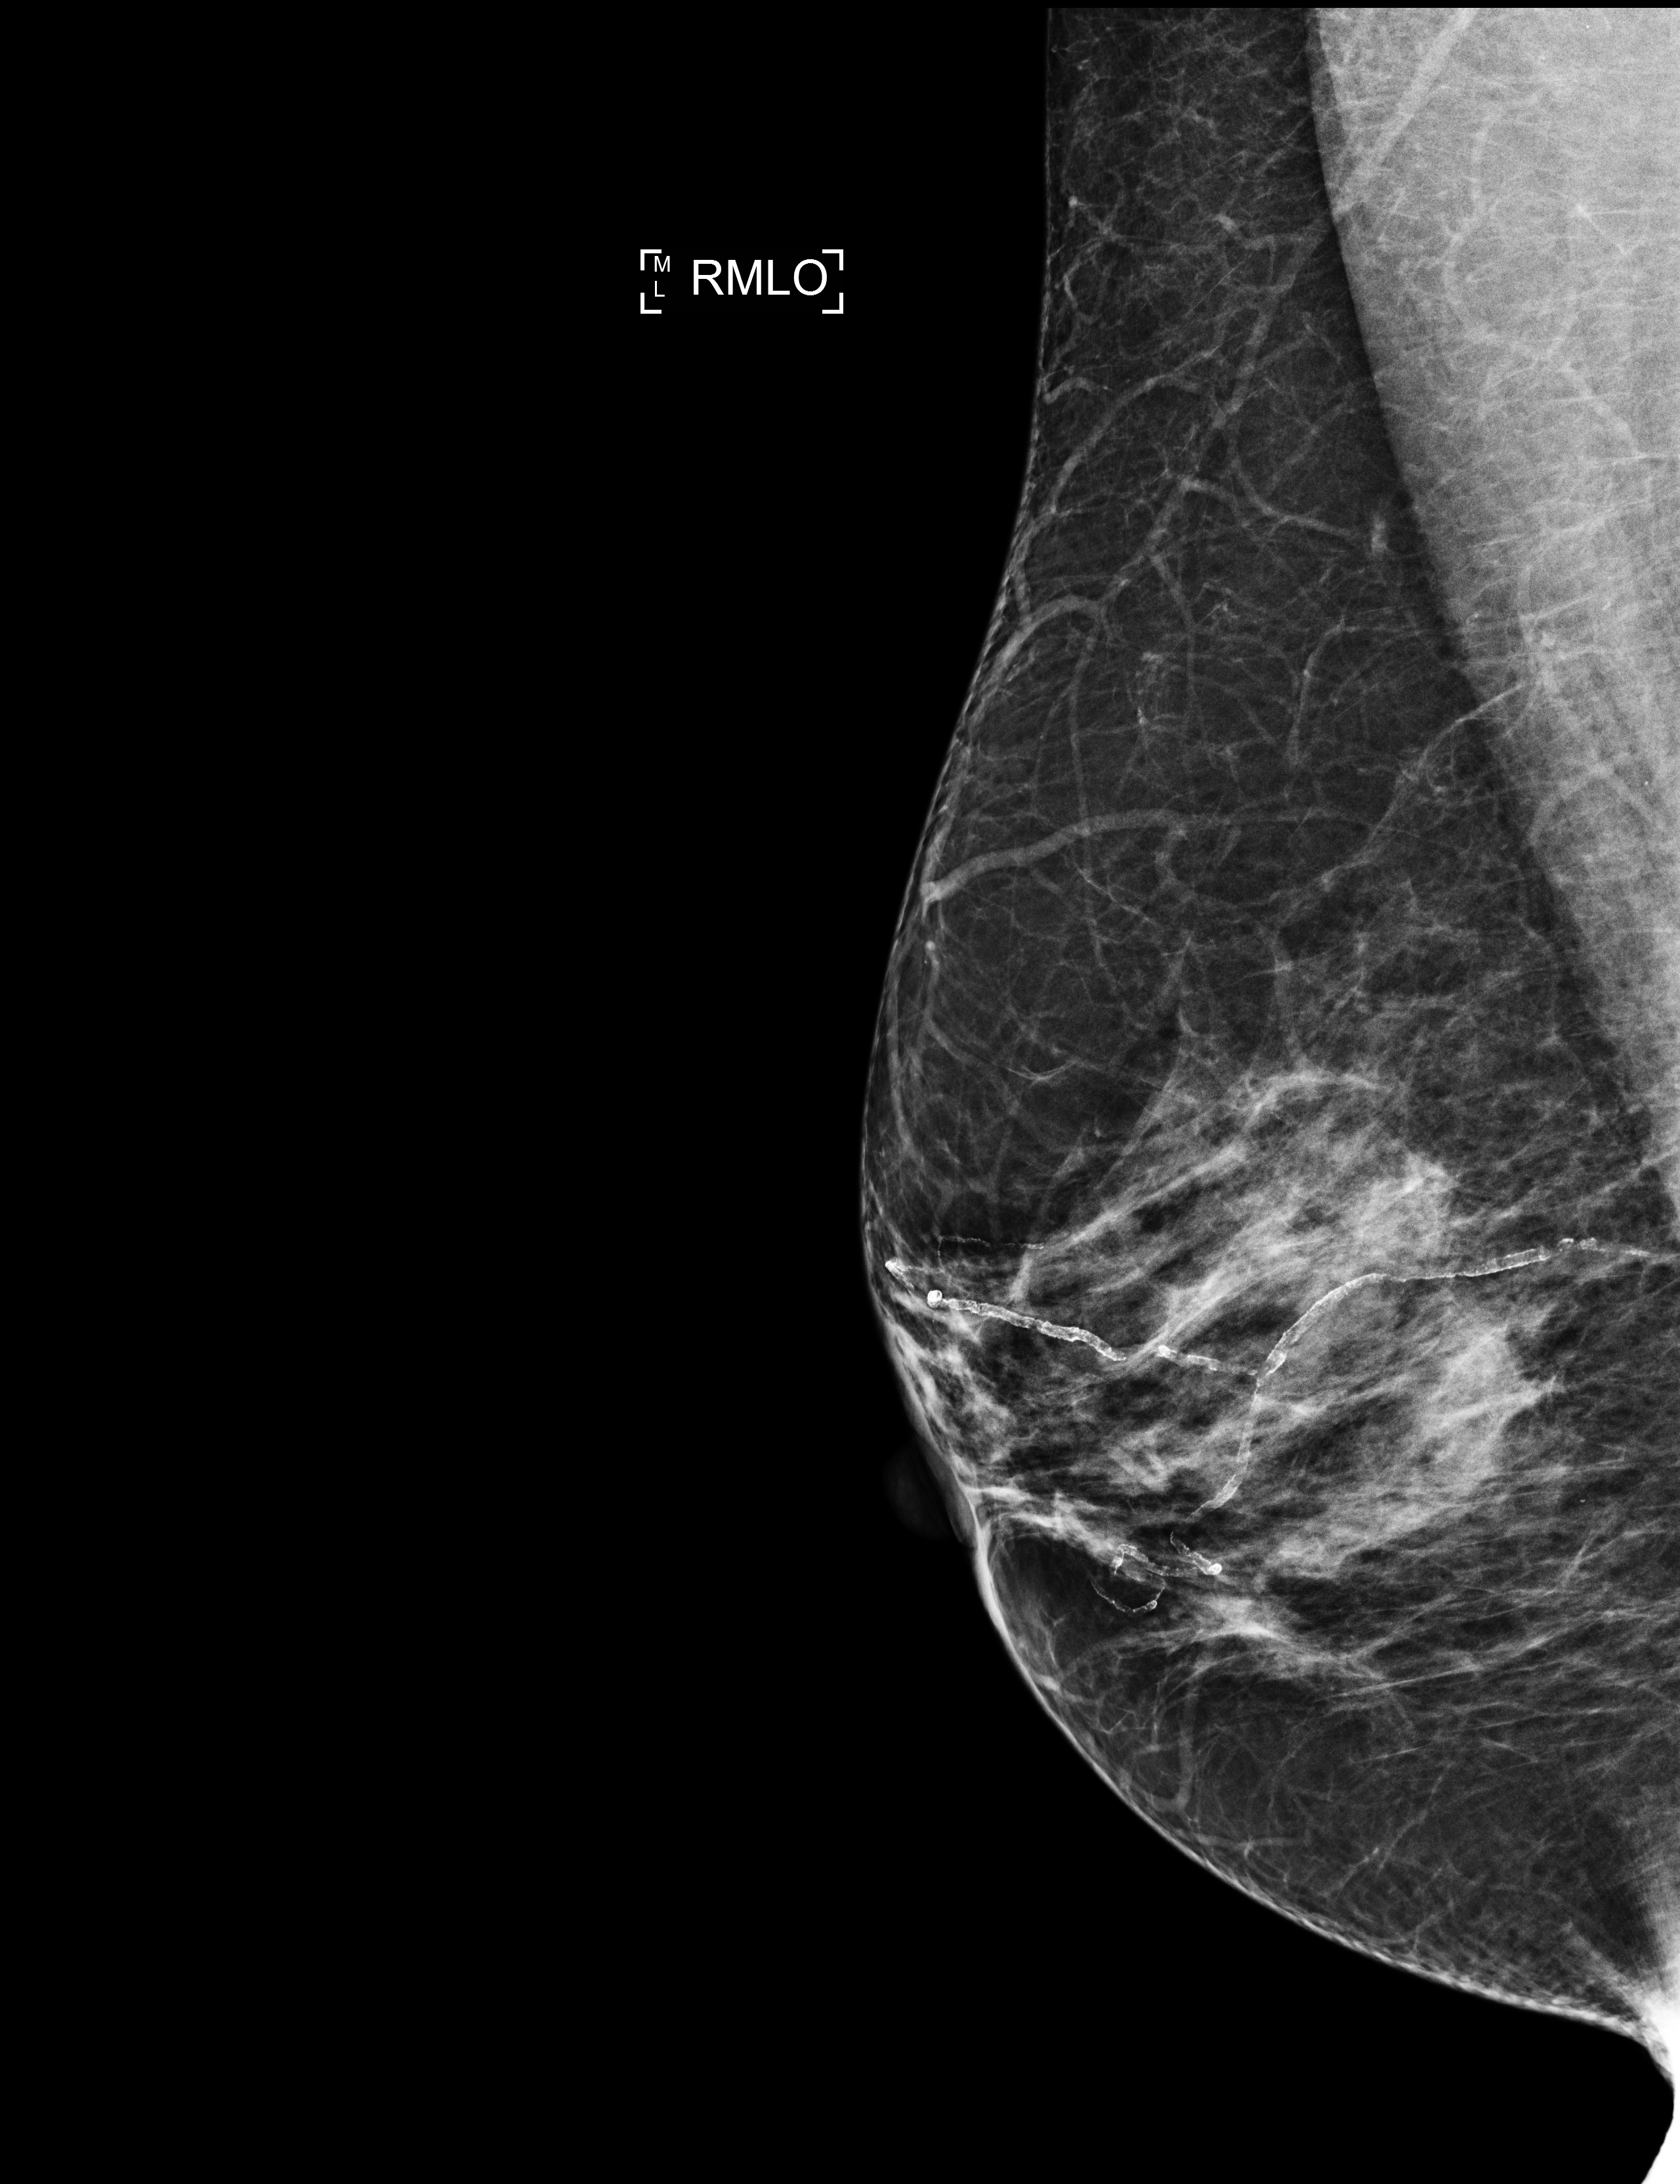
Screening examination; compressed breast thickness 56 mm. Patient aged 60 years (female).
Image type: full-field digital mammogram. Breast: right. Projection: MLO view.